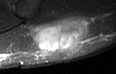
MRI of an extremity soft-tissue mass, one axial slice; STIR; MR volume resampled by the dataset authors to the PET/CT grid (not the native acquisition matrix); 3.27 mm slice thickness; 116 × 74 image matrix, field of view 113 × 72 mm. Male patient. Case-level facts recorded for this patient, not image findings: histological type: pleiomorphic leiomyosarcoma; grade: high; site of the primary tumour: left buttock.
Outlined on this slice (expert contour drawn on MRI and transferred to this co-registered scan by the dataset authors):
- gross tumour volume including surrounding oedema: bounding box <27,17,85,54> (left, top, right, bottom; pixels)
- gross tumour volume (mass): <28,19,83,54>